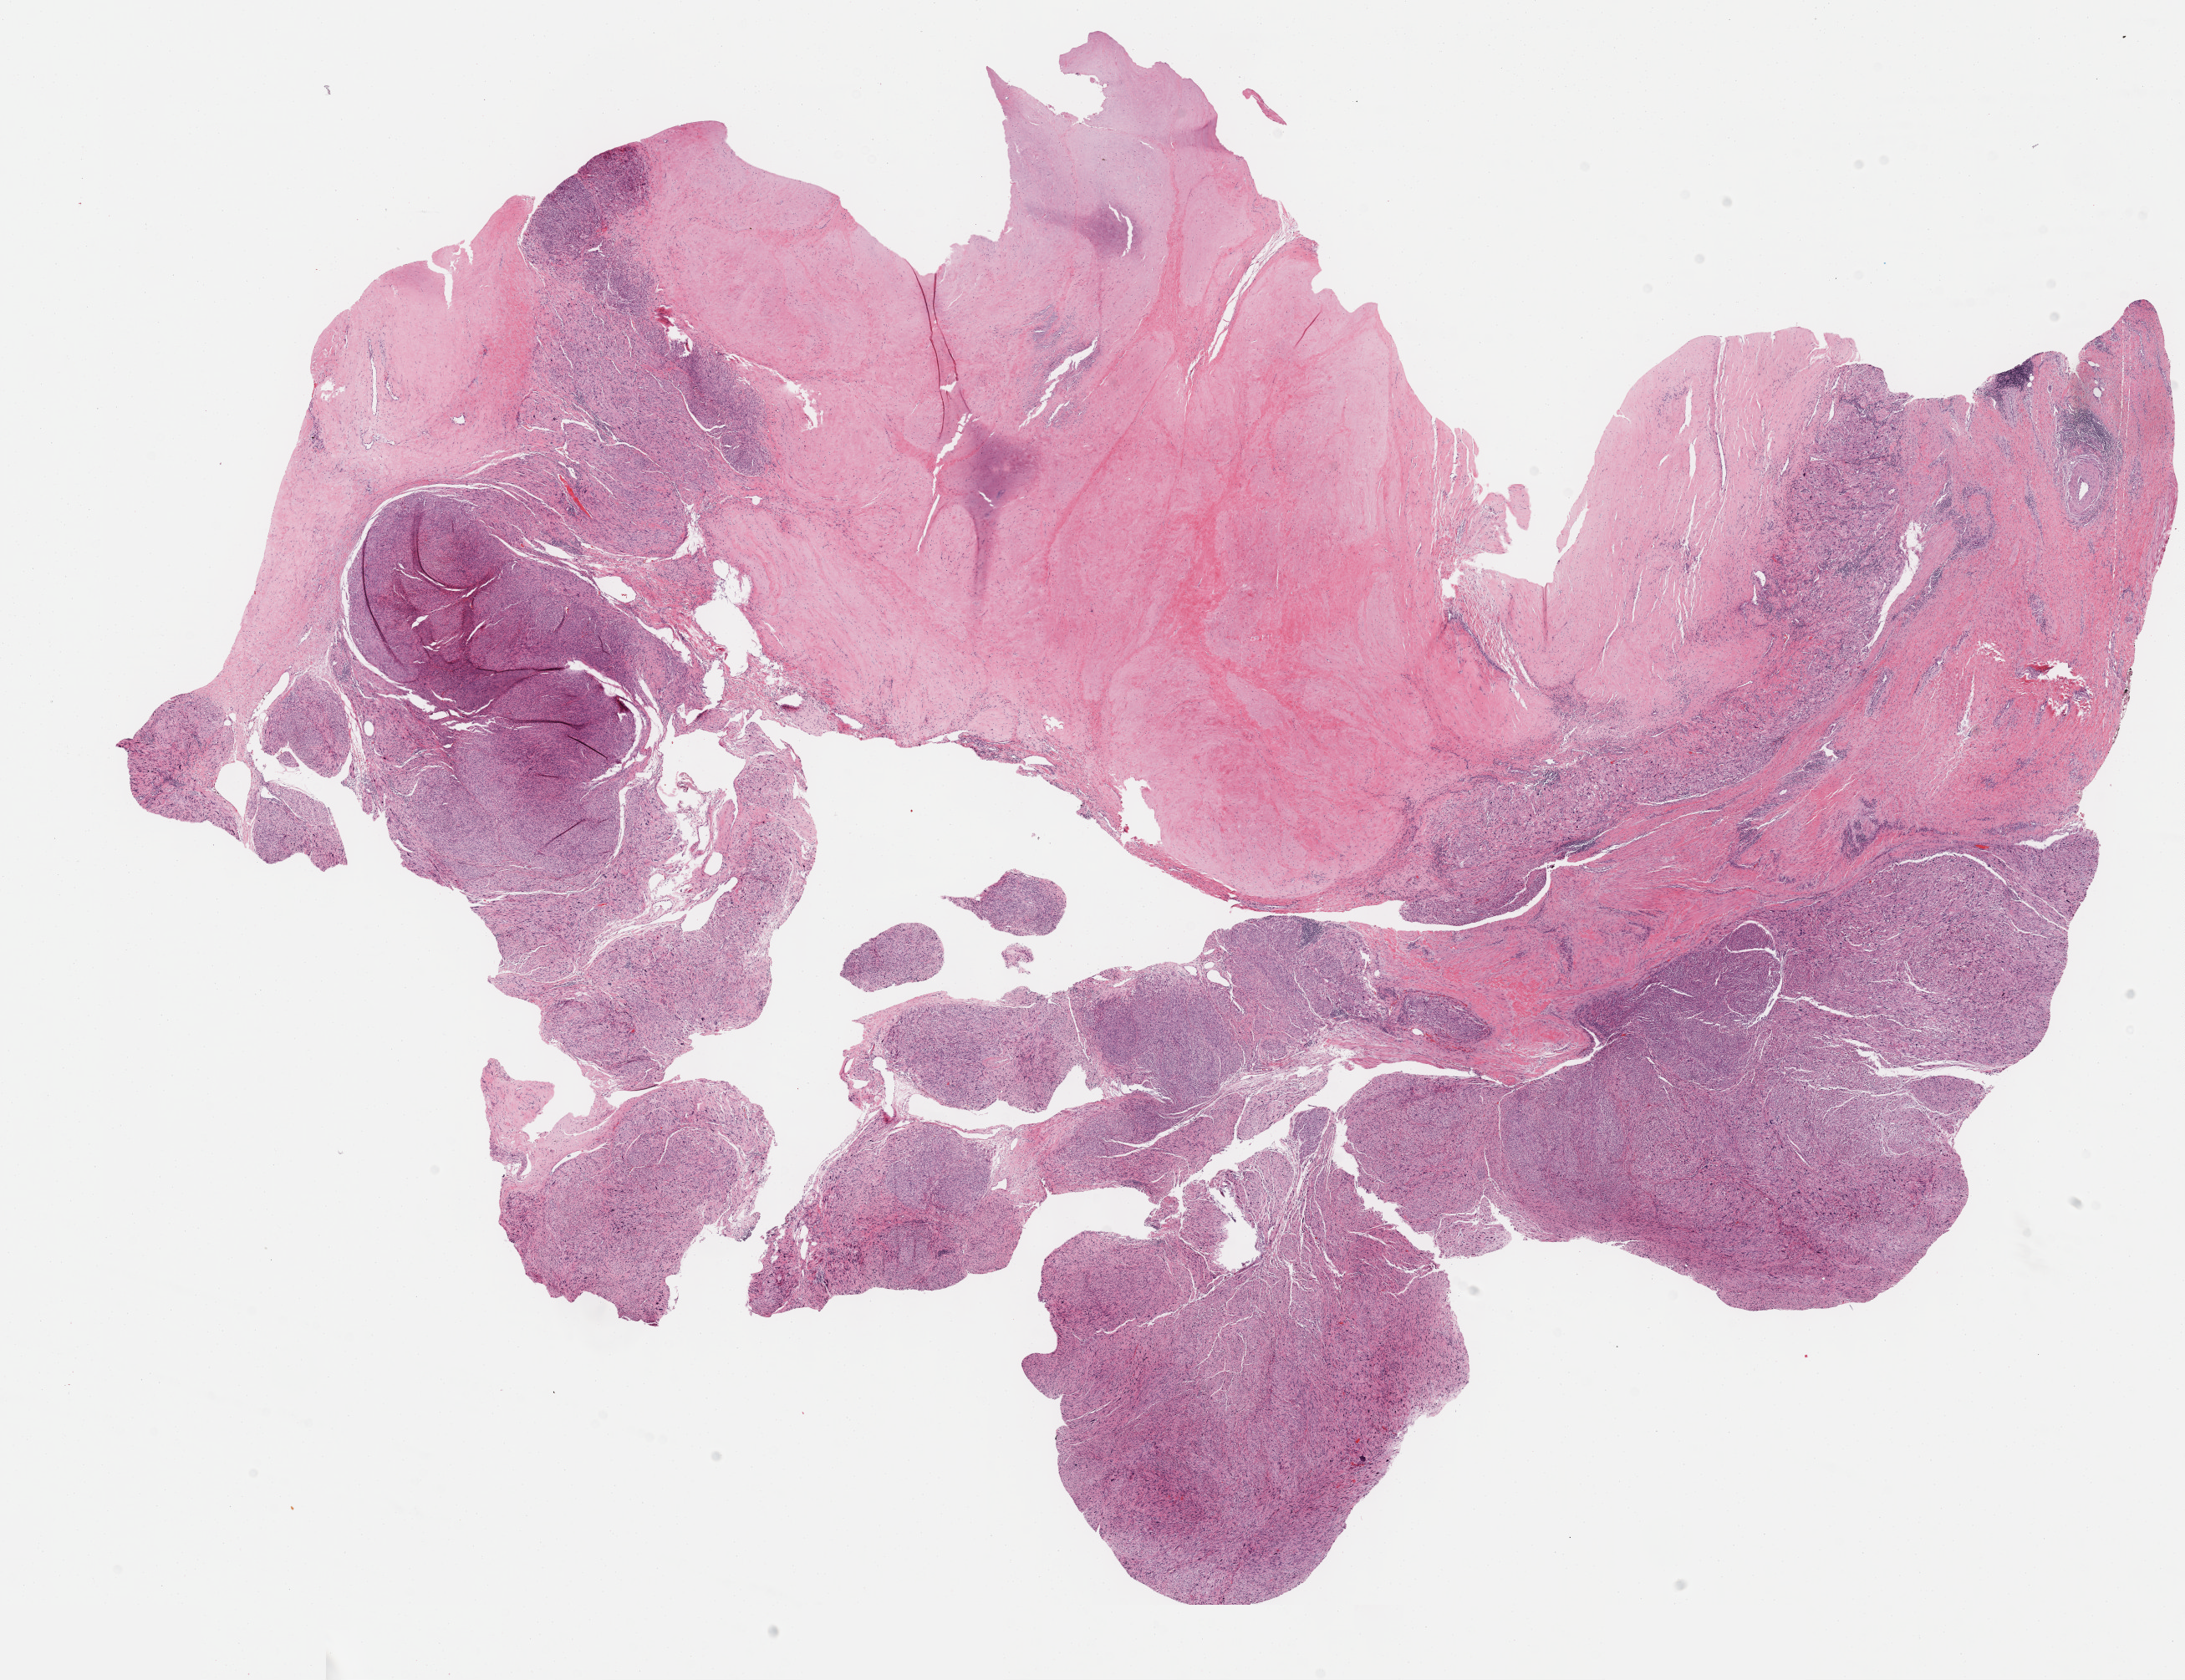
Digitized H&E-stained tissue section (whole slide) — low-resolution overview of the scanned area, about 21.1 x 16.3 mm (slide scanned at 40x), formalin-fixed paraffin-embedded (FFPE) diagnostic section, sample: primary tumour, retroperitoneum and peritoneum. Female patient.
Diagnosis: Leiomyosarcoma, NOS (retroperitoneum).